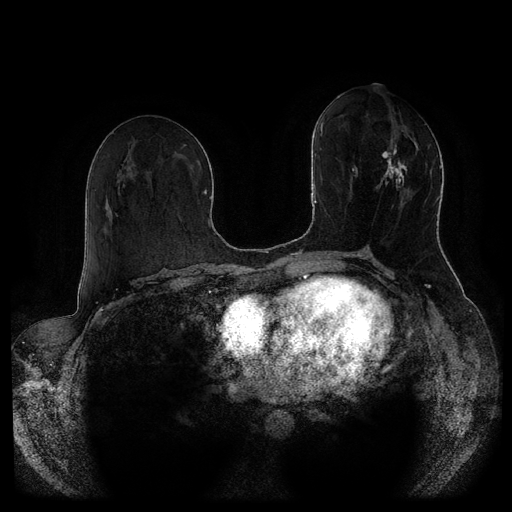
Breast MRI (dynamic contrast-enhanced, multi-phase), one axial slice. Position 46 of 116 along the scan axis. Dynamic contrast-enhanced series, time point 2 of 5 at this slice position (early post-contrast). 1.5 T. TE 2.6 ms, TR 5.3 ms. 2 mm slice thickness. 512 × 512 image matrix. Patient: female, 51 years.
Annotated regions visible in this slice (semi-automatic segmentation, software-assisted and operator-edited):
- breast lesion (labelled 'tumour' in the annotation; benign lesions carry a separate 'benign' label): box from (x=374, y=131) to (x=407, y=218) px